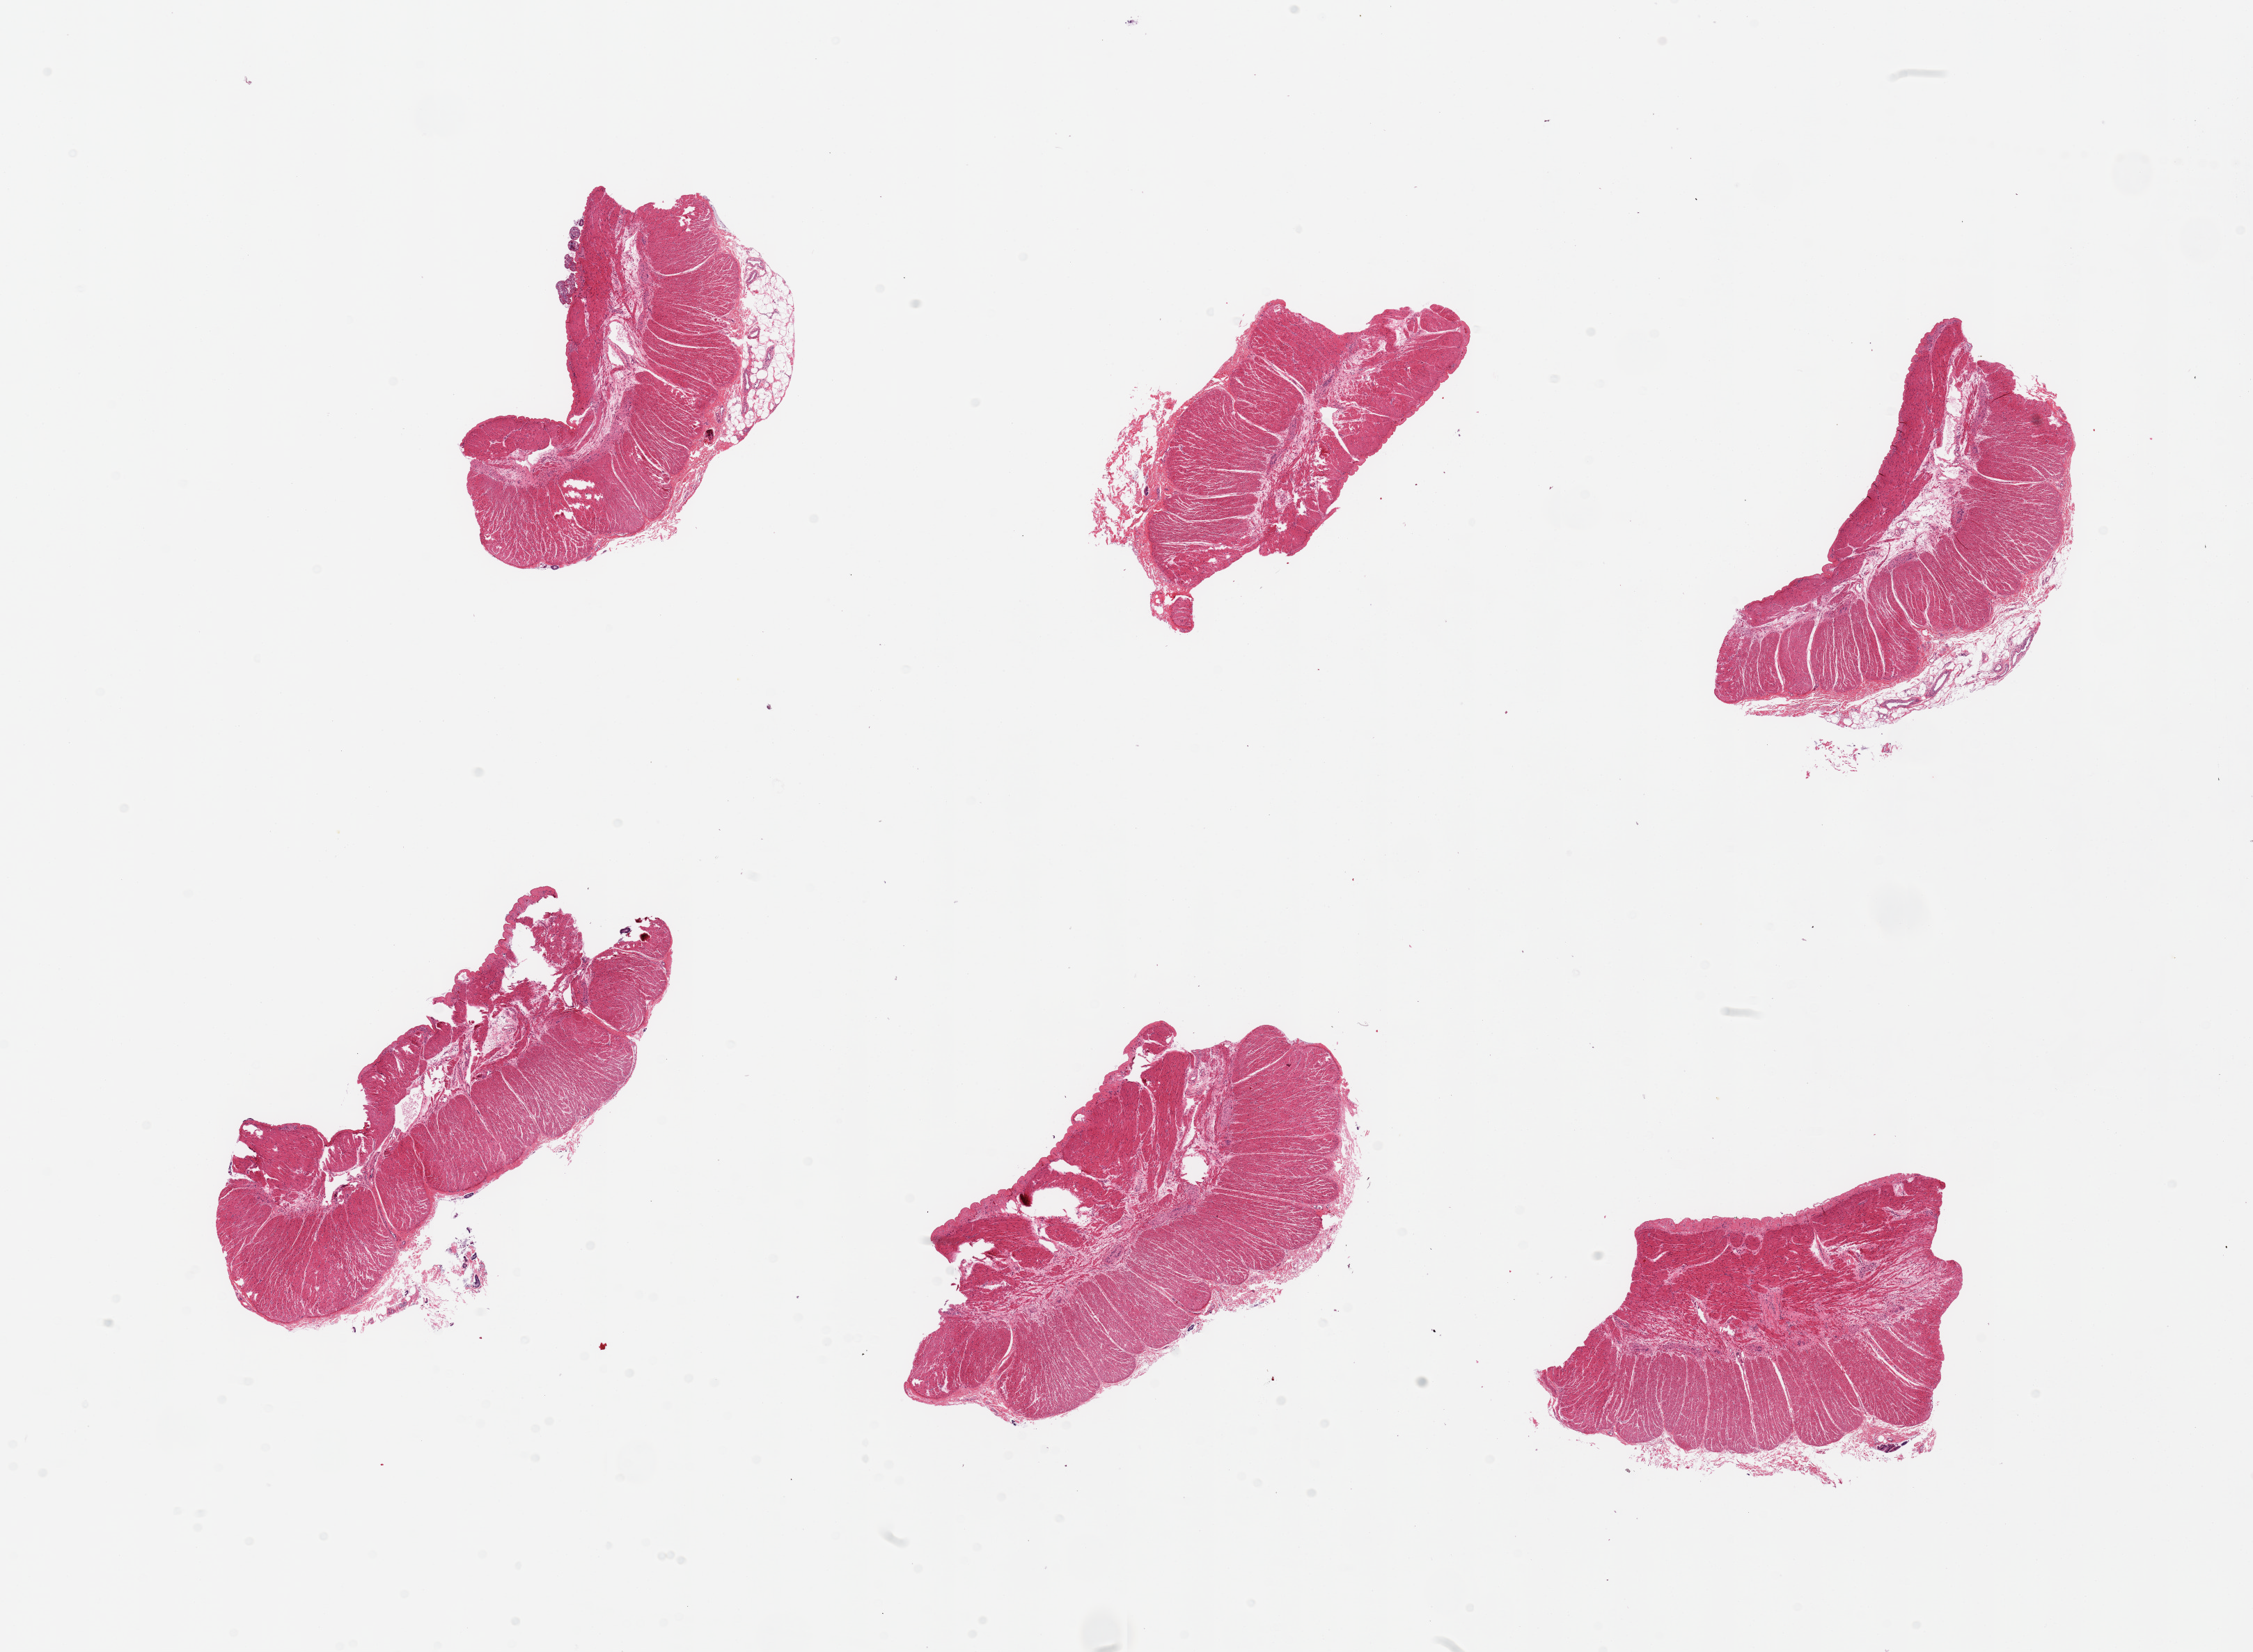
Digitized haematoxylin and eosin-stained section, shown as a low-resolution overview of the whole scanned area (about 25.6 x 18.8 mm, from a 20x scan); PAXgene-fixed, paraffin-embedded tissue; section of sigmoid colon (target tissue); donor tissue sample. Donor: female.
Reviewer comment on this tissue sample: 6 pieces.